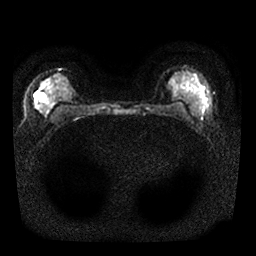
Breast MRI, one axial slice. Position 14 of 25 along the scan axis. Diffusion-weighted series; image 2 of 4 stored at this slice position (different b-values; order by instance number). 1.5 T. 4 mm slice thickness. 256 × 256 image matrix. Female patient.
Annotated regions visible in this slice (manually delineated by an expert):
- tumour on diffusion-weighted imaging: bounding box (x1, y1, x2, y2) in pixels: (41, 95, 43, 98)